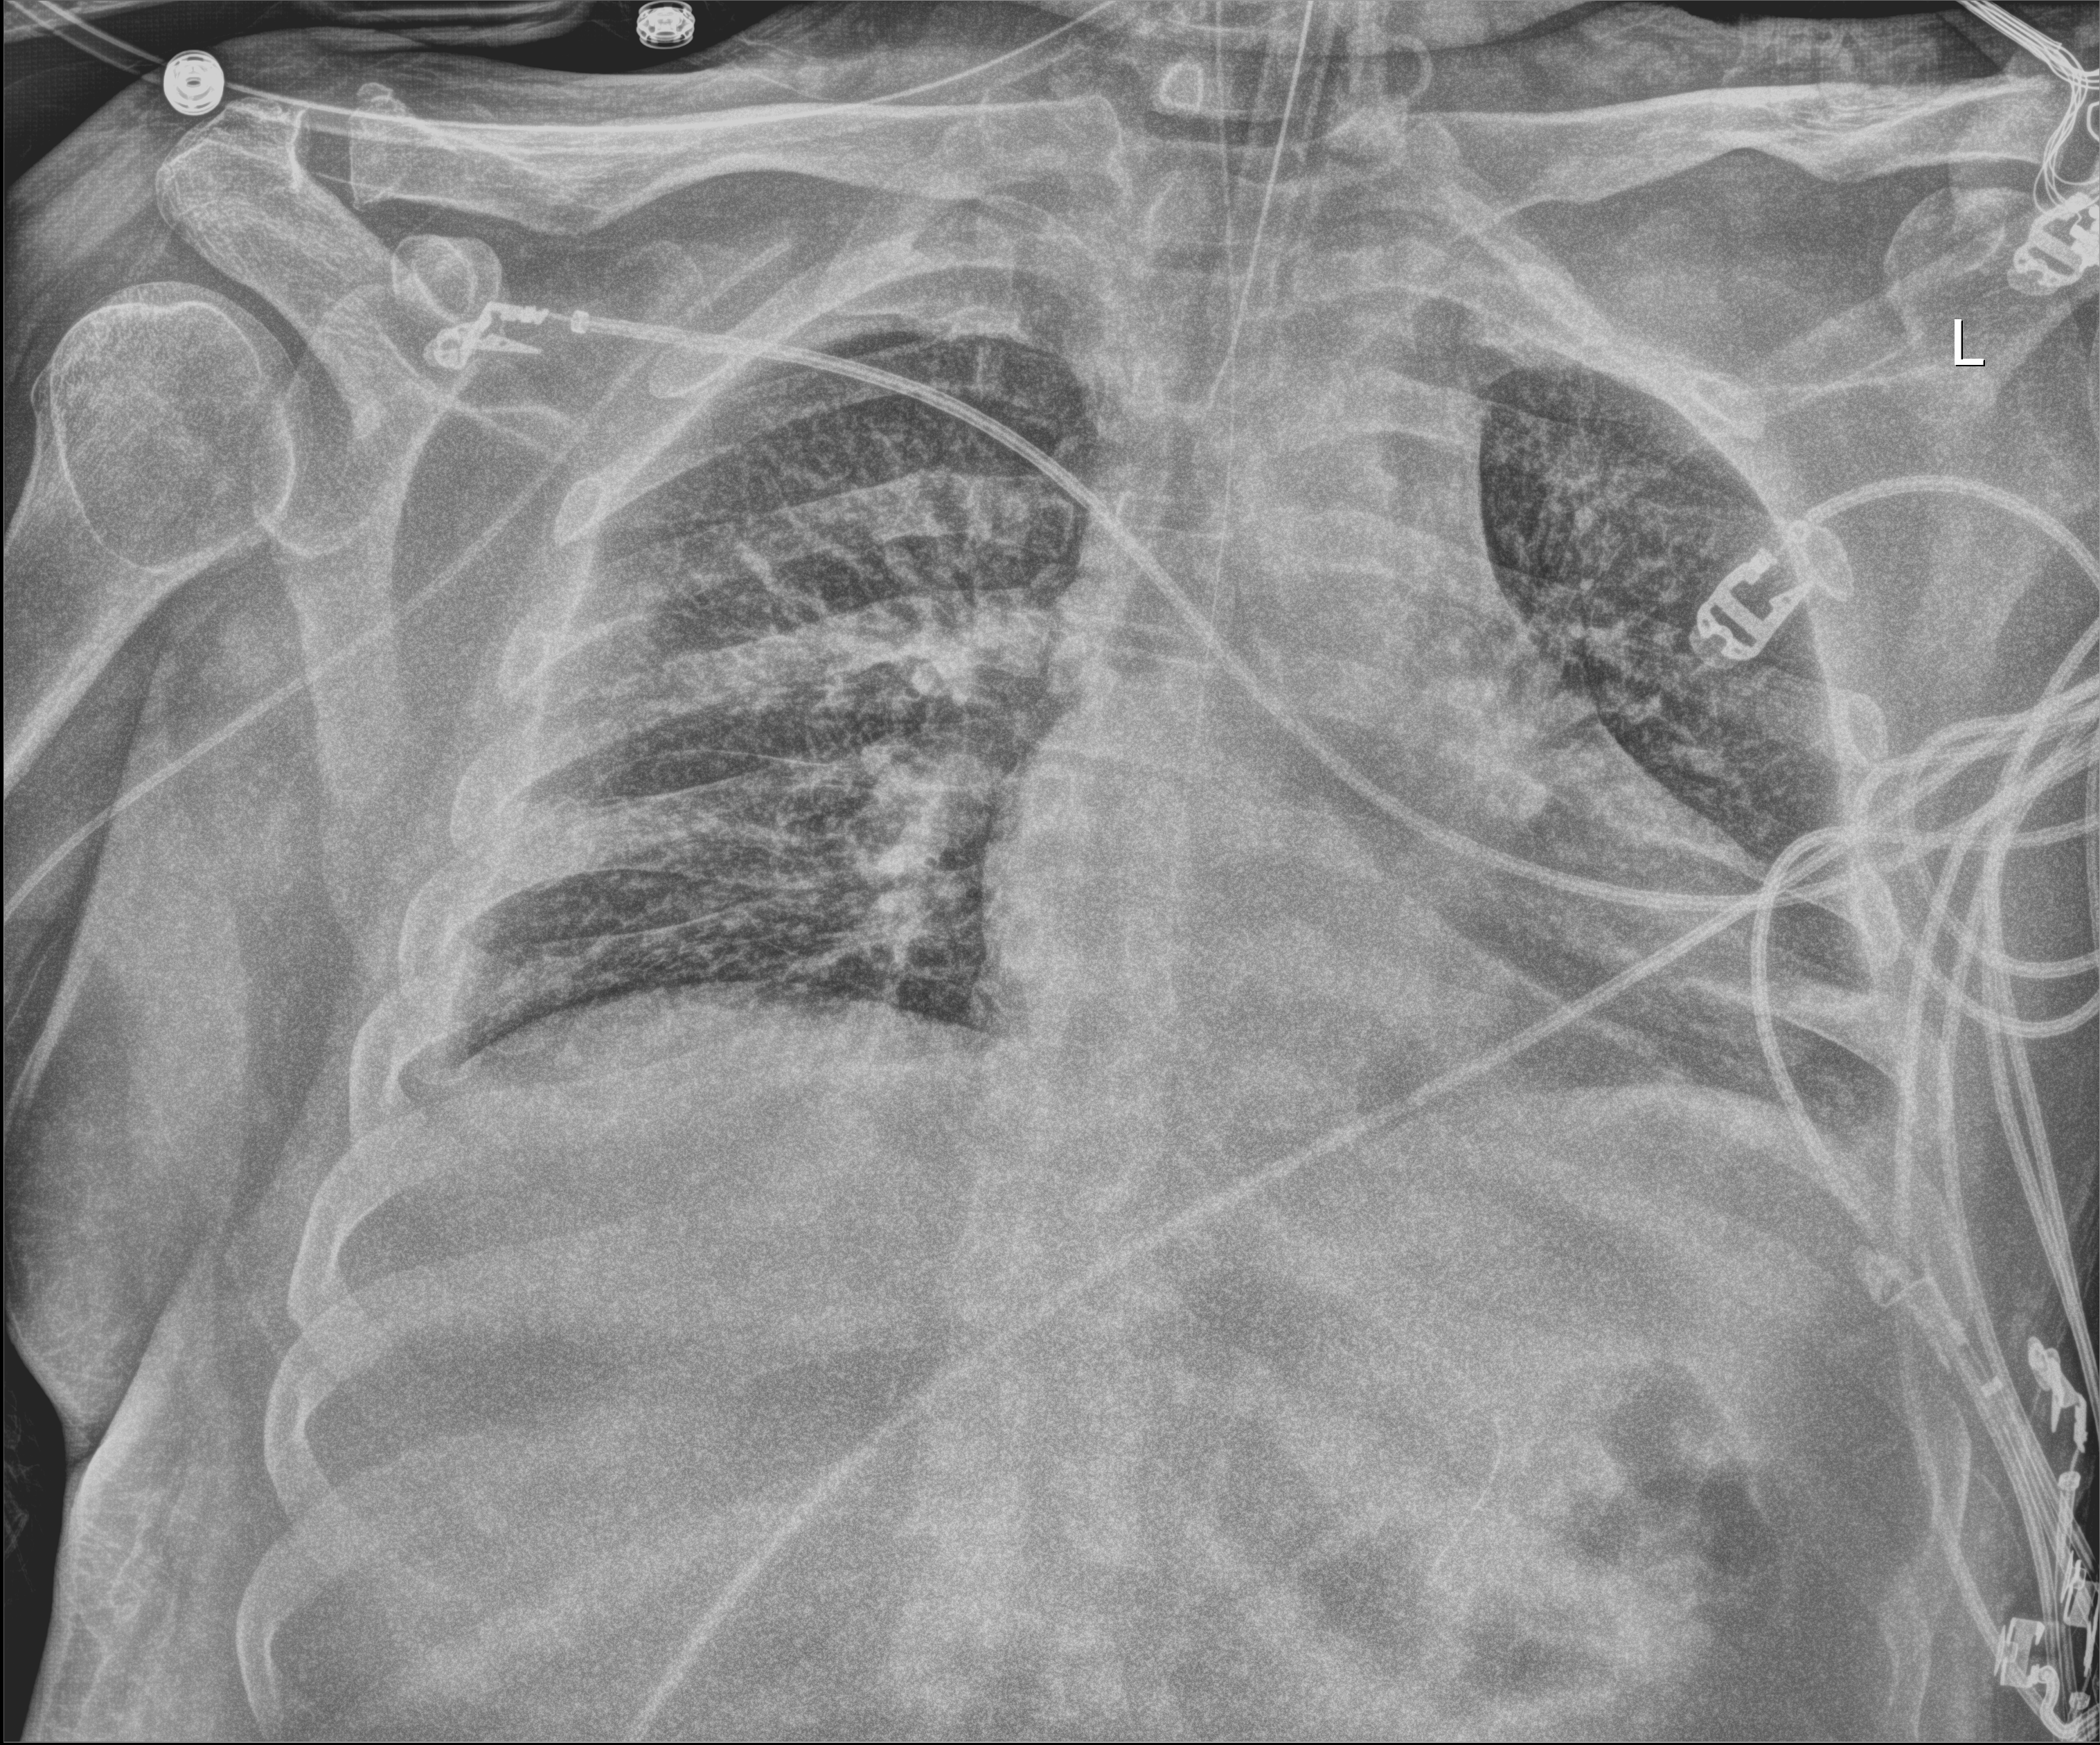
Bedside chest radiograph (digital radiography); anteroposterior (AP) projection. Male patient hospitalised with COVID-19, age 18–59 years.
From the hospital-stay record, not from the radiograph (when in the stay this image was taken is not recorded):
- mechanically ventilated during this hospital stay: yes
- admitted to intensive care during this hospital stay: yes